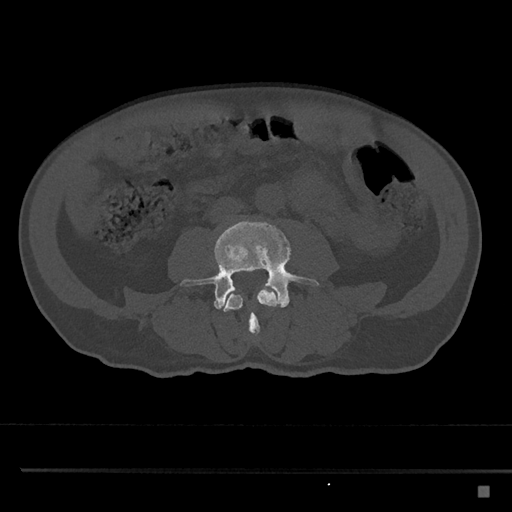
CT including the spine, one axial slice; position 658 of 797 along the scan axis; reconstruction kernel Br40s/3; bone window (W 1800 / L 400 HU); 512 × 512 image matrix, field of view 391 × 391 mm. Patient: male, 59 years. From the clinical record (not read from this slice): primary cancer: prostate.
Outlined on this slice (semi-automatic segmentation, software-assisted and operator-edited):
- L3 vertebra: bounding box <221,283,281,335> (left, top, right, bottom; pixels)
- L4 vertebra: <180,220,320,309>